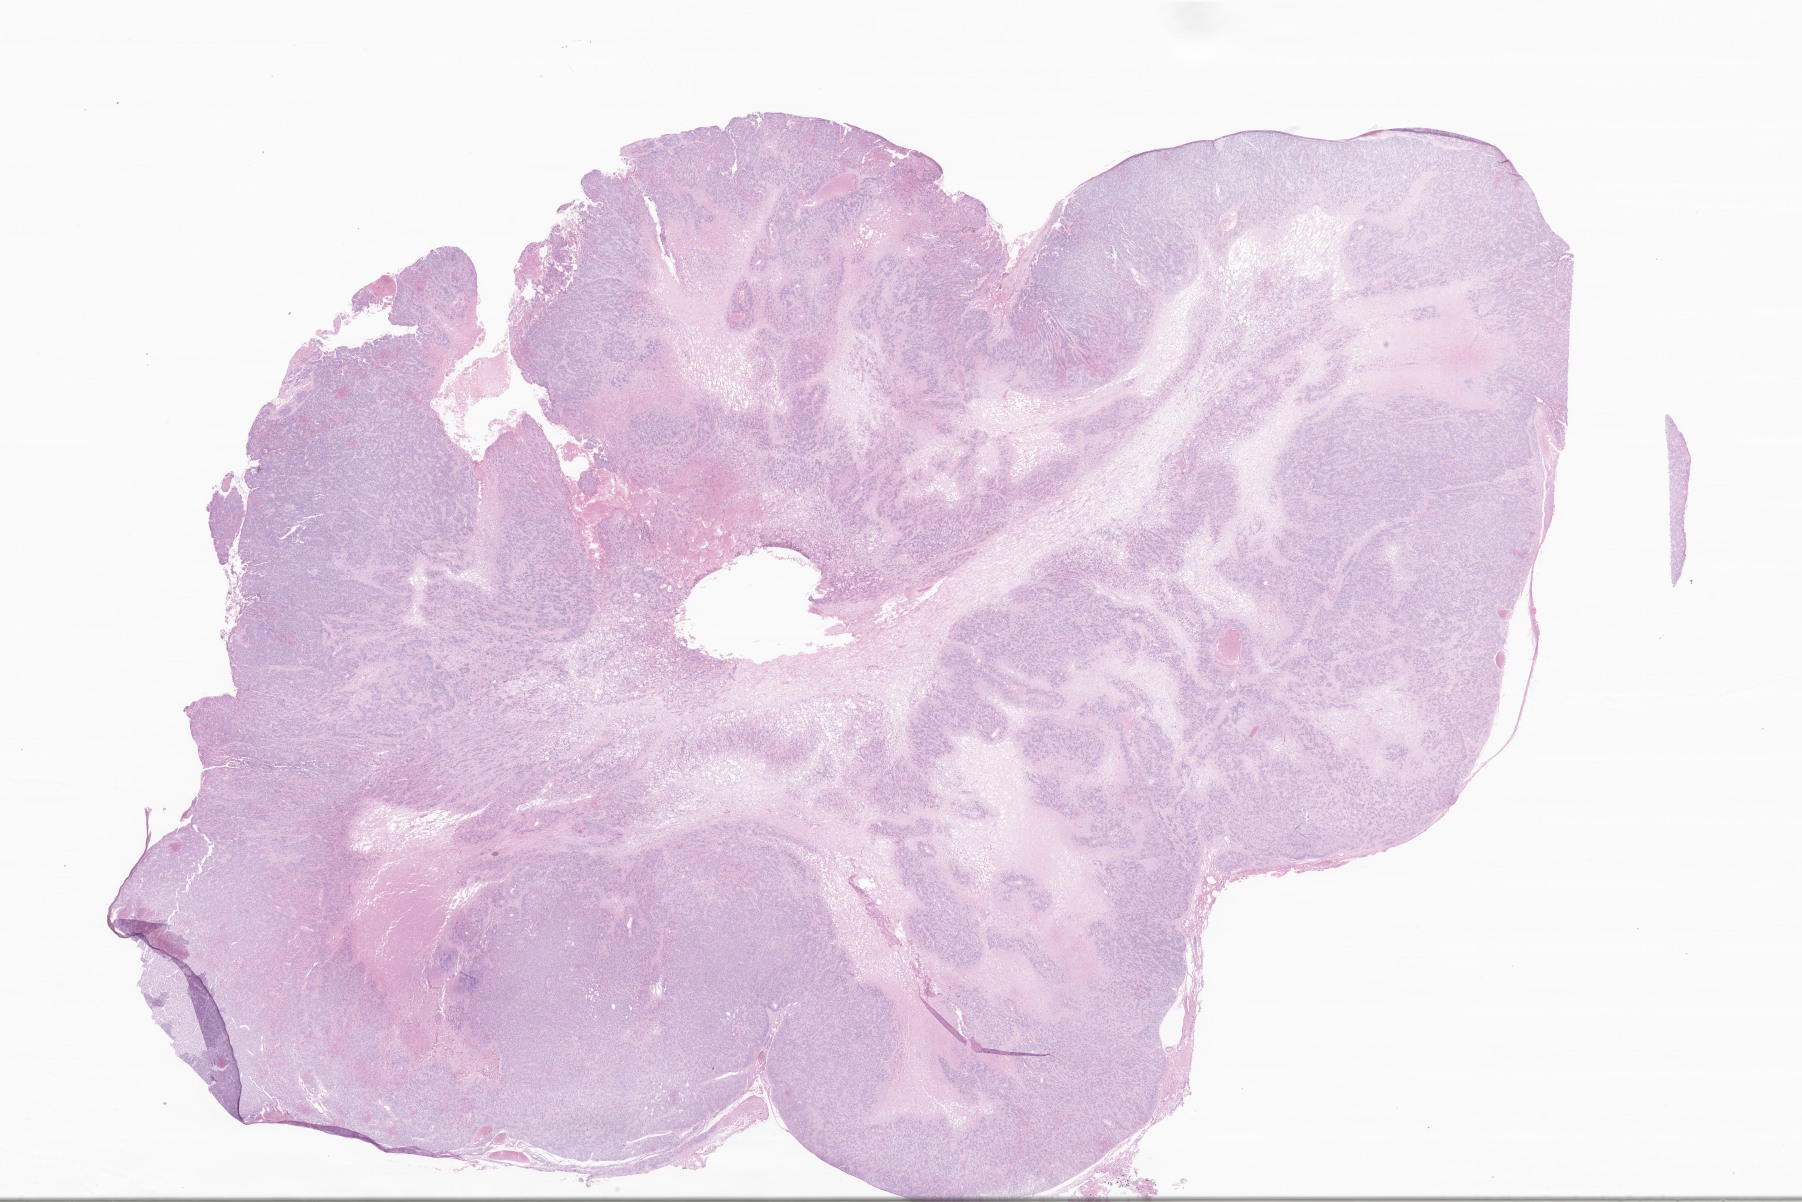
Digitized haematoxylin and eosin-stained section of tumor tissue from the brain — whole scanned area (about 30.4 x 20.3 mm) shown as a low-resolution overview. FFPE section. Male patient, age 113 months.
* recorded diagnosis: Ependymoma, NOS